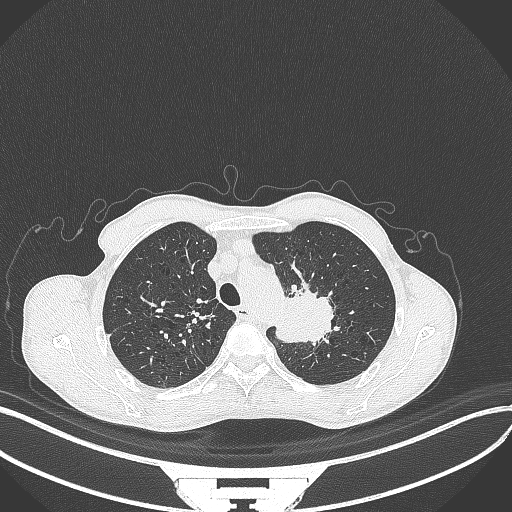
Chest CT, one axial slice; slice 334 of 386 in the series (ordered by position); reconstruction kernel B70f; 120 kVp; lung window (W 1500 / L -600 HU); 512 × 512 image matrix, field of view 400 × 400 mm. Patient: male, 65 years. Case-level facts recorded for this patient, not image findings: clinical TNM (as recorded): T2b N0 M0; histopathological grade: G2.
Outlined on this slice (bounding box drawn by a radiologist):
- lung tumour (recorded histology: adenocarcinoma): bounding box <269,287,338,346> (left, top, right, bottom; pixels)